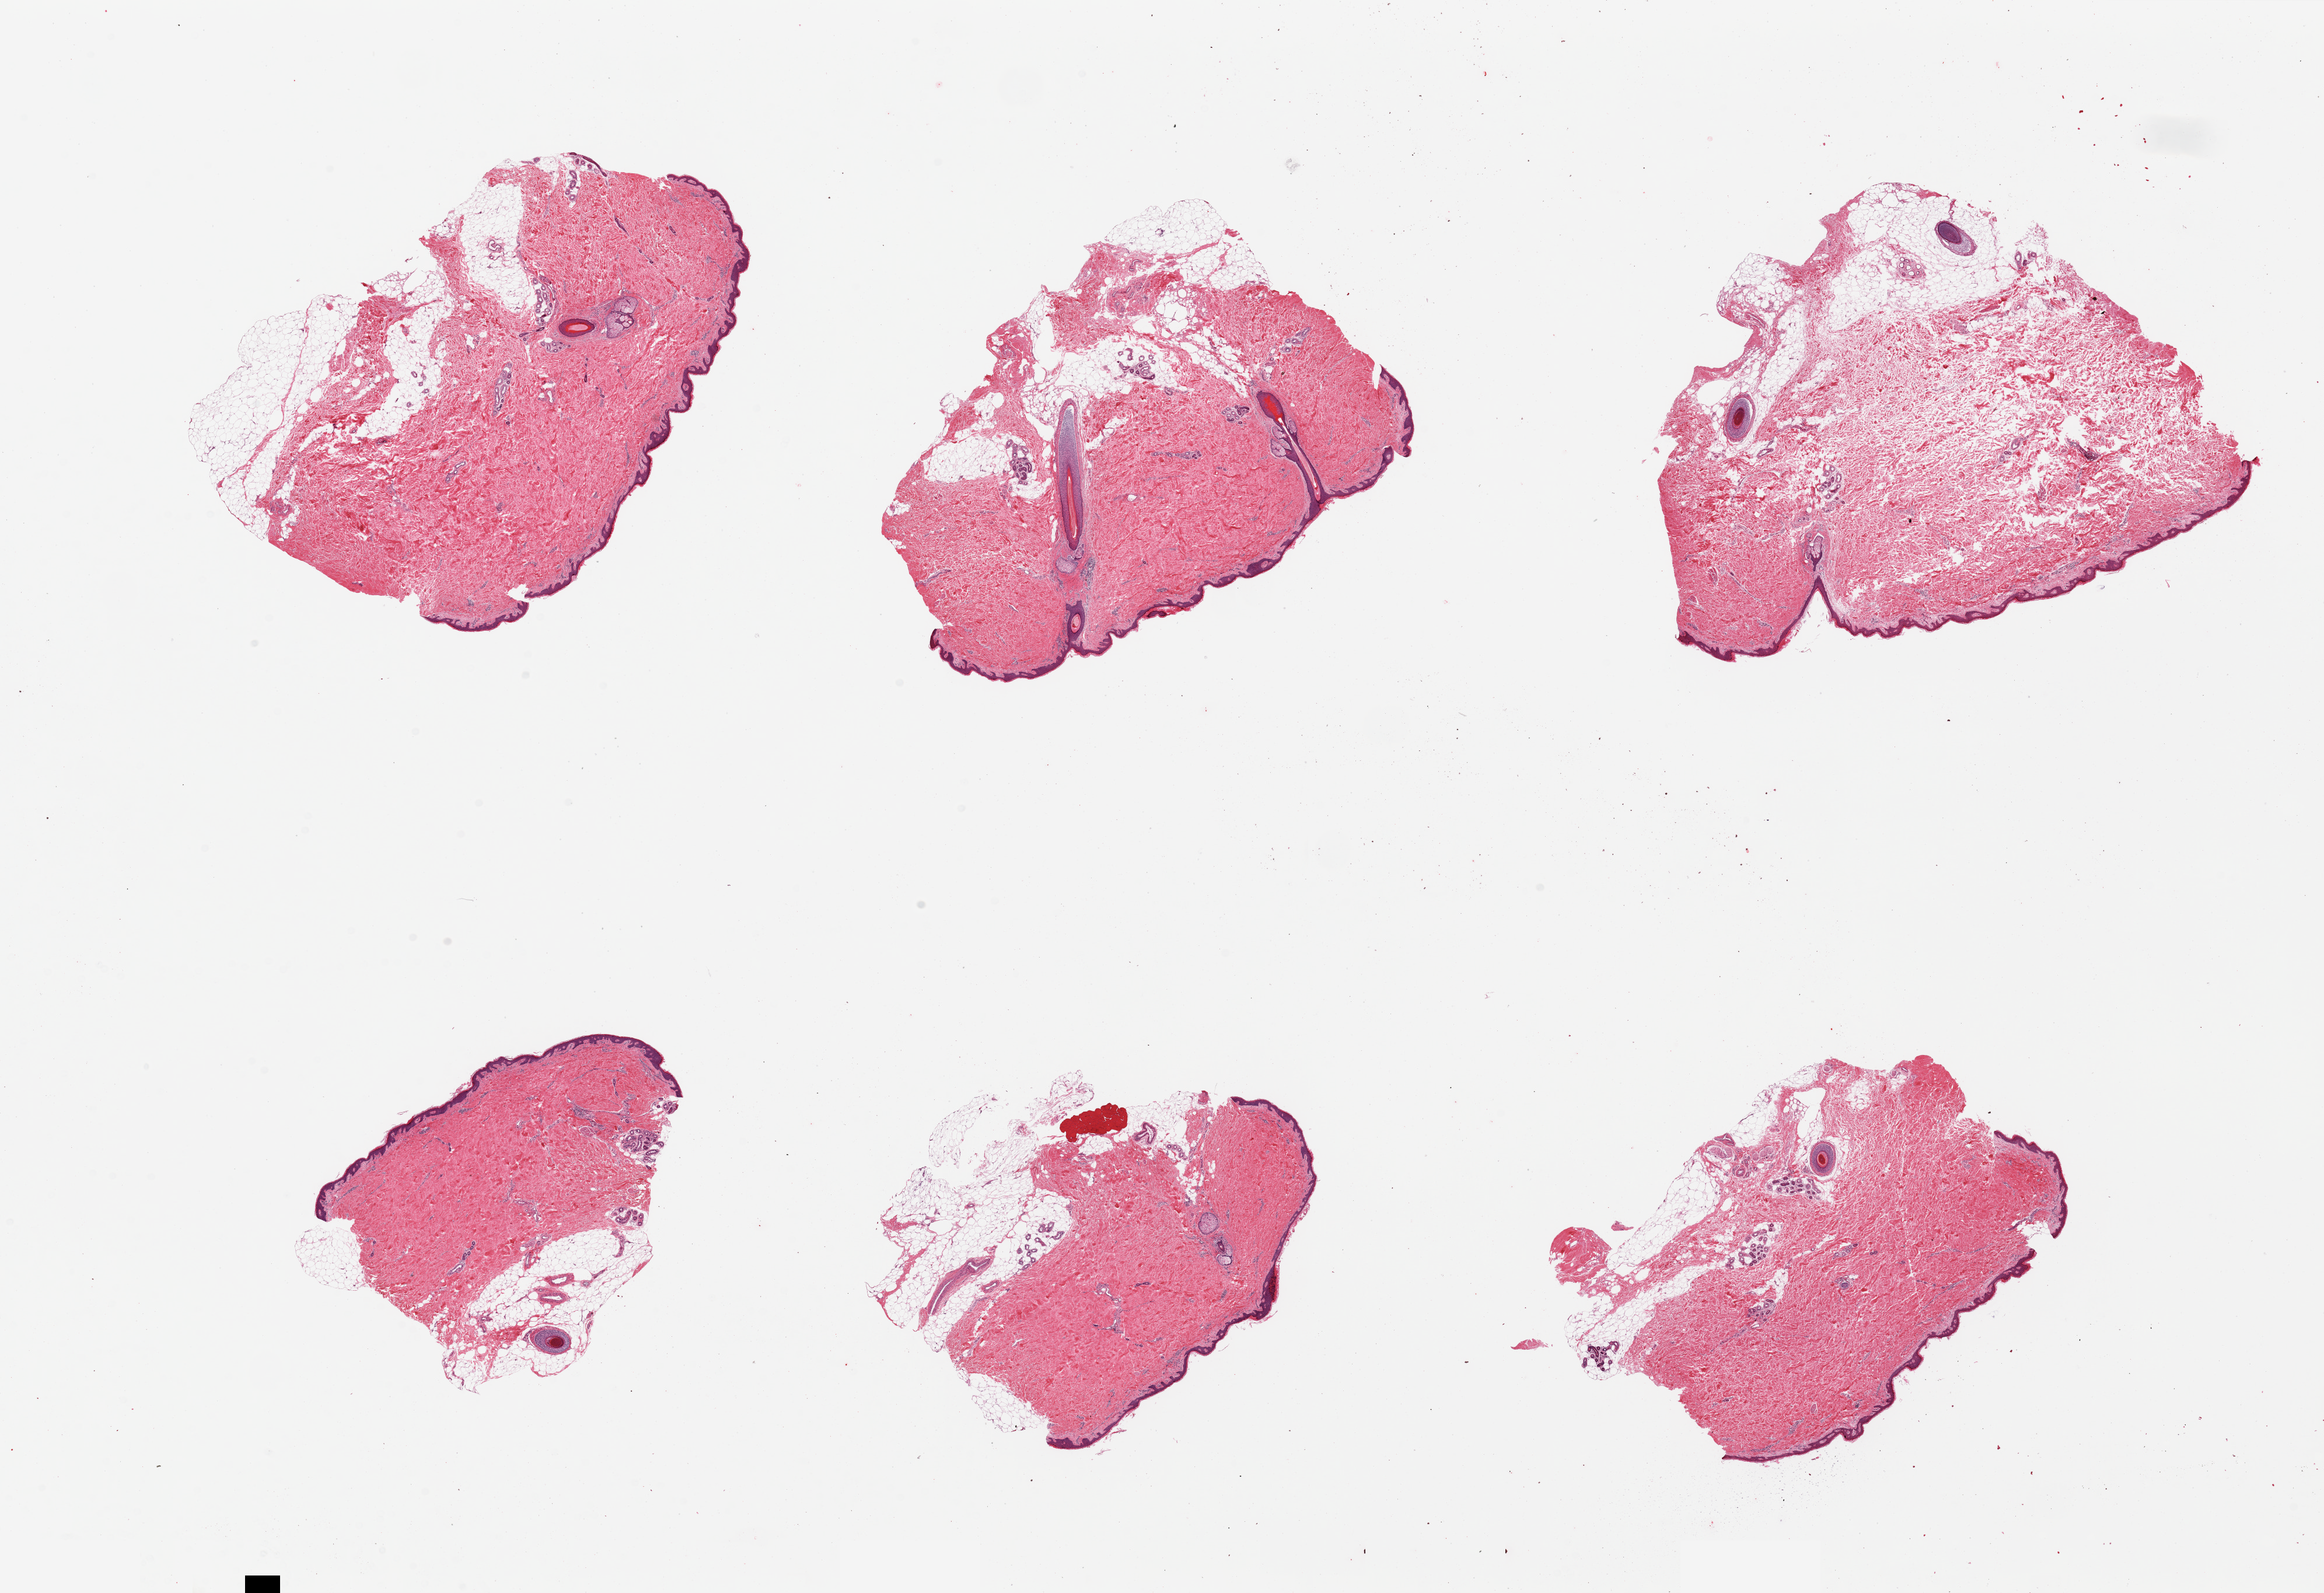
Hematoxylin and eosin (H&E) whole-slide image, brightfield — shown as a low-resolution overview of the whole scanned area (about 31.5 x 21.6 mm, from a 20x scan). PAXgene-fixed paraffin-embedded (PFPE) section. Target tissue: skin of suprapubic region. Tissue donor sample. Donor sex: male.
* reviewer comment on this tissue sample: 6 pieces. All with subcutaneous fat up to 2mm